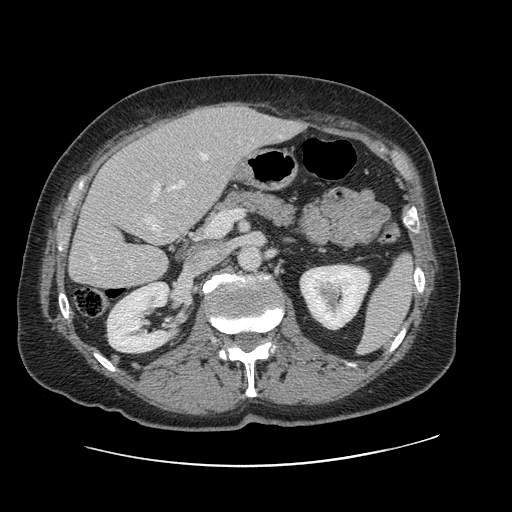
Contrast-enhanced abdominal CT, one axial slice; slice 49 of 138 in the series (ordered by position); soft-tissue window (W 400 / L 40 HU); 512 × 512 image matrix. Male patient, age 71 years. From the clinical record (not read from this slice): diagnosis: colorectal cancer liver metastases, imaged before liver resection; multiple liver metastases: no; largest metastasis: 3.3 cm; disease in both lobes: no.
Annotated regions visible in this slice (expert manual segmentation):
- hepatic veins: bounding box (x1, y1, x2, y2) in pixels: (90, 154, 227, 270)
- liver: (70, 104, 300, 290)
- planned liver remnant (the part of the liver to remain after resection): (70, 140, 198, 290)
- portal vein (with intrahepatic branches): (151, 182, 160, 202)